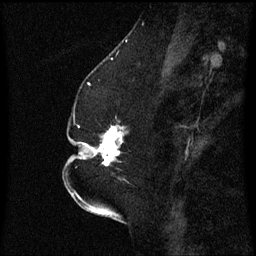
Breast MRI (dynamic contrast-enhanced), one sagittal slice; slice 22 of 60 in the series (ordered by position); dynamic contrast-enhanced series, image 2 of 3 at this slice position (ordered by acquisition); 1.5 T; TE 4.2 ms, TR 8.4 ms; 2.3 mm slice thickness; 256 × 256 image matrix, field of view 200 × 200 mm. Patient: female, 52 years. From the clinical record (not read from this slice): setting: breast cancer imaged before/during neoadjuvant chemotherapy; receptor status: HR-positive, HER2-negative.
Outlined on this slice (semi-automatic segmentation, software-assisted and operator-edited):
- analysis volume of interest (the breast-tissue region the enhancement analysis was run in; not a lesion): bounding box (x1, y1, x2, y2) in pixels: (75, 126, 126, 181)
- tumour enhancement mask (voxels above the 70 % enhancement threshold inside the analysis volume of interest): (78, 126, 126, 167)